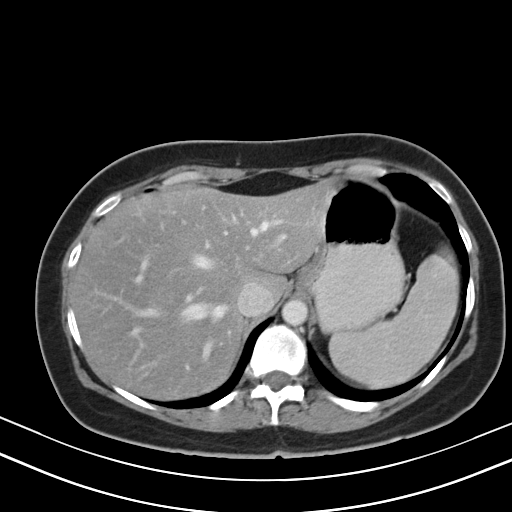
Contrast-enhanced abdominal CT, one axial slice. Position 37 of 47 along the scan axis. Reconstruction kernel B40s. 130 kVp. Intravenous contrast given. Soft-tissue window (W 400 / L 40 HU). 5 mm slice thickness. 512 × 512 image matrix, field of view 350 × 350 mm. Female patient. From the clinical record (not read from this slice): diagnosis: colorectal cancer liver metastases, imaged before liver resection; multiple liver metastases: no; largest metastasis: 3.5 cm; disease in both lobes: no.
Structures marked on this image (expert manual segmentation):
- hepatic veins: bounding box <105,216,281,355> (left, top, right, bottom; pixels)
- liver: <73,184,331,398>
- planned liver remnant (the part of the liver to remain after resection): <74,184,331,398>
- portal vein (with intrahepatic branches): <128,234,287,371>